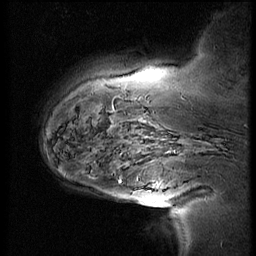
Breast MRI (dynamic contrast-enhanced), one sagittal slice. Position 14 of 60 along the scan axis. 4 images stored at this slice position (order not interpretable as contrast timing). 1.5 T. TE 4.2 ms, TR 9 ms. 256 × 256 image matrix. Patient: female, 56 years. From the clinical record (not read from this slice): setting: breast cancer imaged before/during neoadjuvant chemotherapy; receptor status: HER2-positive.
Structures marked on this image (semi-automatically segmented with operator editing):
- analysis volume of interest (the breast-tissue region the enhancement analysis was run in; not a lesion): bounding box <110,138,192,201> (left, top, right, bottom; pixels)
- tumour enhancement mask (voxels above the 140 % enhancement threshold inside the analysis volume of interest): <119,181,121,183>